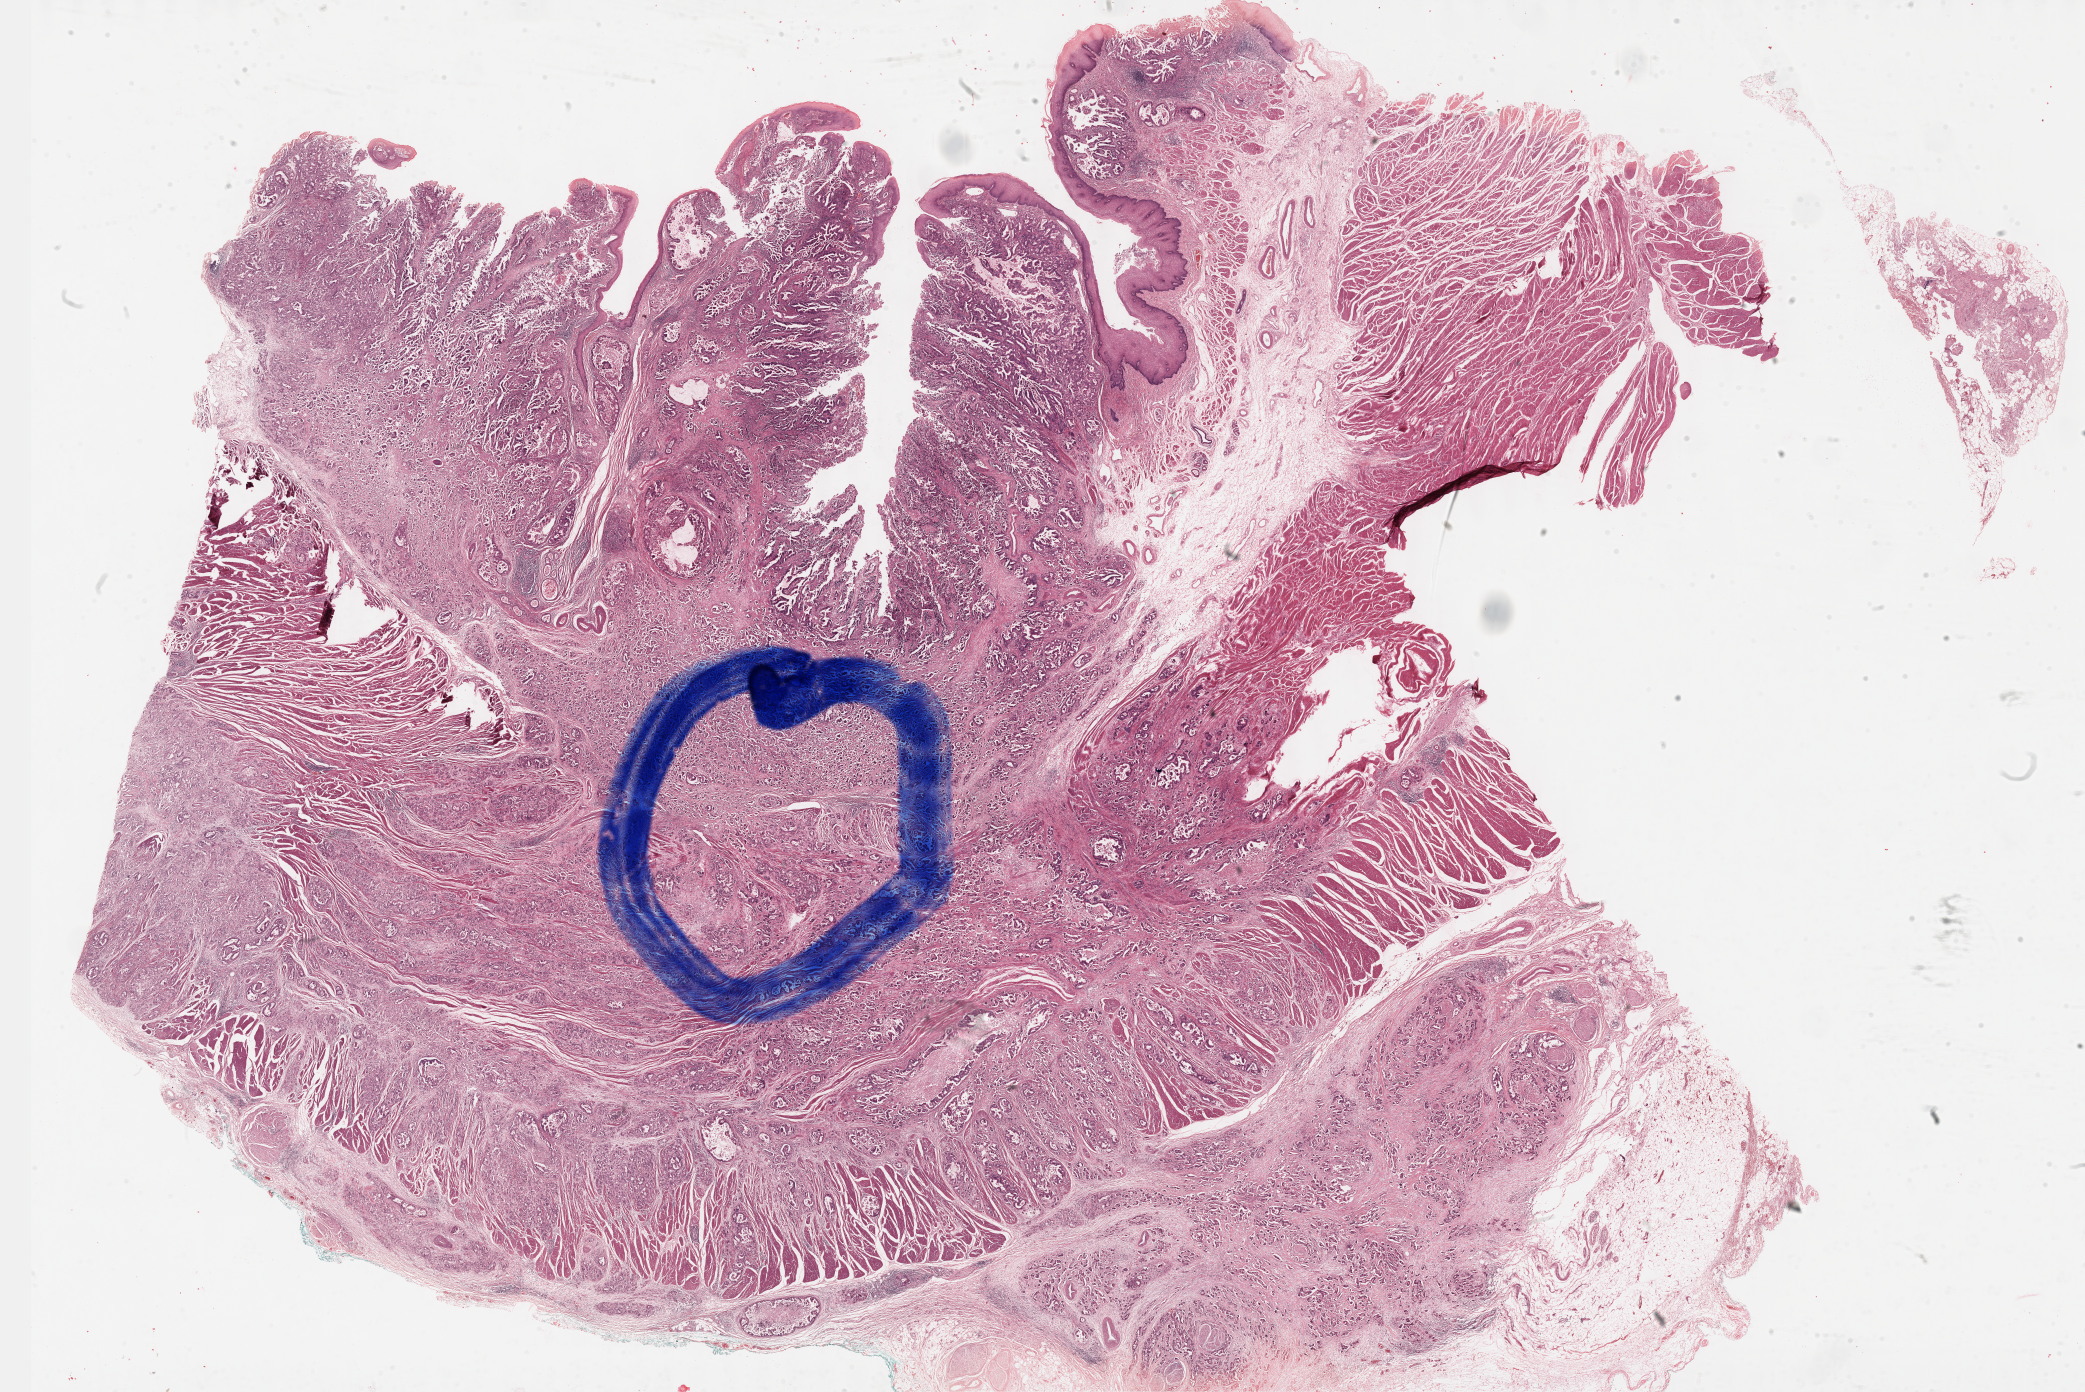
Hematoxylin and eosin (H&E) stained whole-slide image, a low-resolution overview of the entire scanned area, about 33.7 x 22.5 mm (acquisition: 40x scan); formalin-fixed paraffin-embedded (FFPE) diagnostic section; sample: primary tumour, esophagus. Male, age 67 years at initial diagnosis. Histologic grade: G3 (poorly differentiated).
TNM: T3 N1 M0. Histologic diagnosis: Adenocarcinoma, NOS (lower third of esophagus). Lymph nodes positive (case pathology): 7 of 8 examined. AJCC pathologic stage: III.